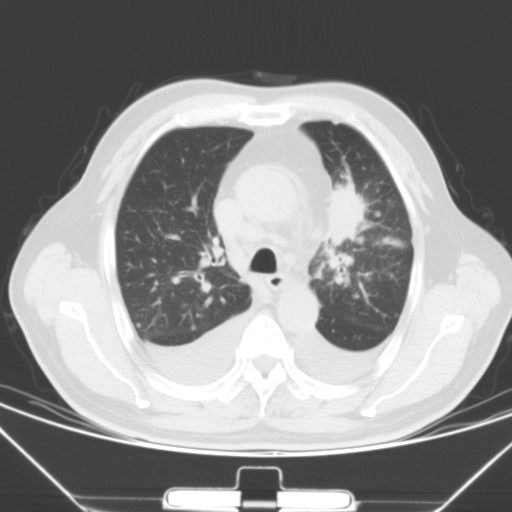
Chest CT, one axial slice. Slice 44 of 66 in the series (ordered by position). 120 kVp. Lung window (W 1500 / L -600 HU). 5 mm slice thickness. 512 × 512 image matrix. Male patient, age 66 years. From the clinical record (not read from this slice): clinical TNM (as recorded): T1c N0 M0.
Structures marked on this image (rectangle marked by the reading radiologist):
- lung tumour (recorded histology: adenocarcinoma): bounding box [x1, y1, x2, y2] px = [323, 177, 364, 247]